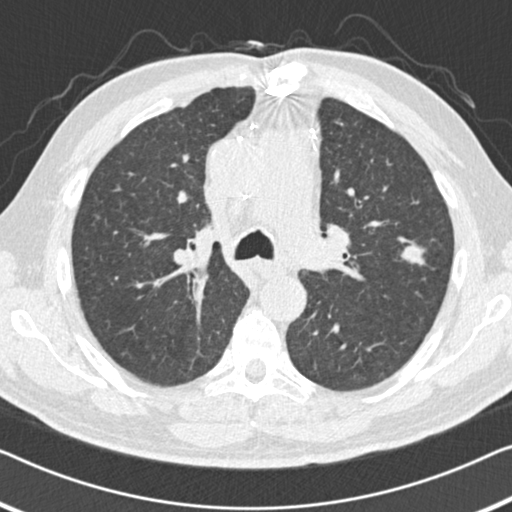
Low-dose screening chest CT, axial slice. First (baseline) screen. Lung window (W 1500 / L -600 HU). 2 mm slice thickness. 120 kVp. Slice 54 of 155 in the series. Male participant, aged 64 years at enrolment.
Expert-annotated lung lesion, bounding box <384,229,440,280> (left, top, right, bottom; pixels). The screening reader recorded 2 non-calcified nodules or masses ≥4 mm on this exam (left upper lobe, right middle lobe); which of them this box marks is not recorded. Official screen result: positive, change unspecified: nodule(s) >= 4 mm or enlarging nodule(s), mass(es), or other non-specific abnormalities suspicious for lung cancer. Participant outcome: lung cancer diagnosed 133 days after this screen — adenocarcinoma, NOS, left upper lobe, poorly differentiated (G3), stage IA (AJCC 6th edition), 15 mm at pathology.